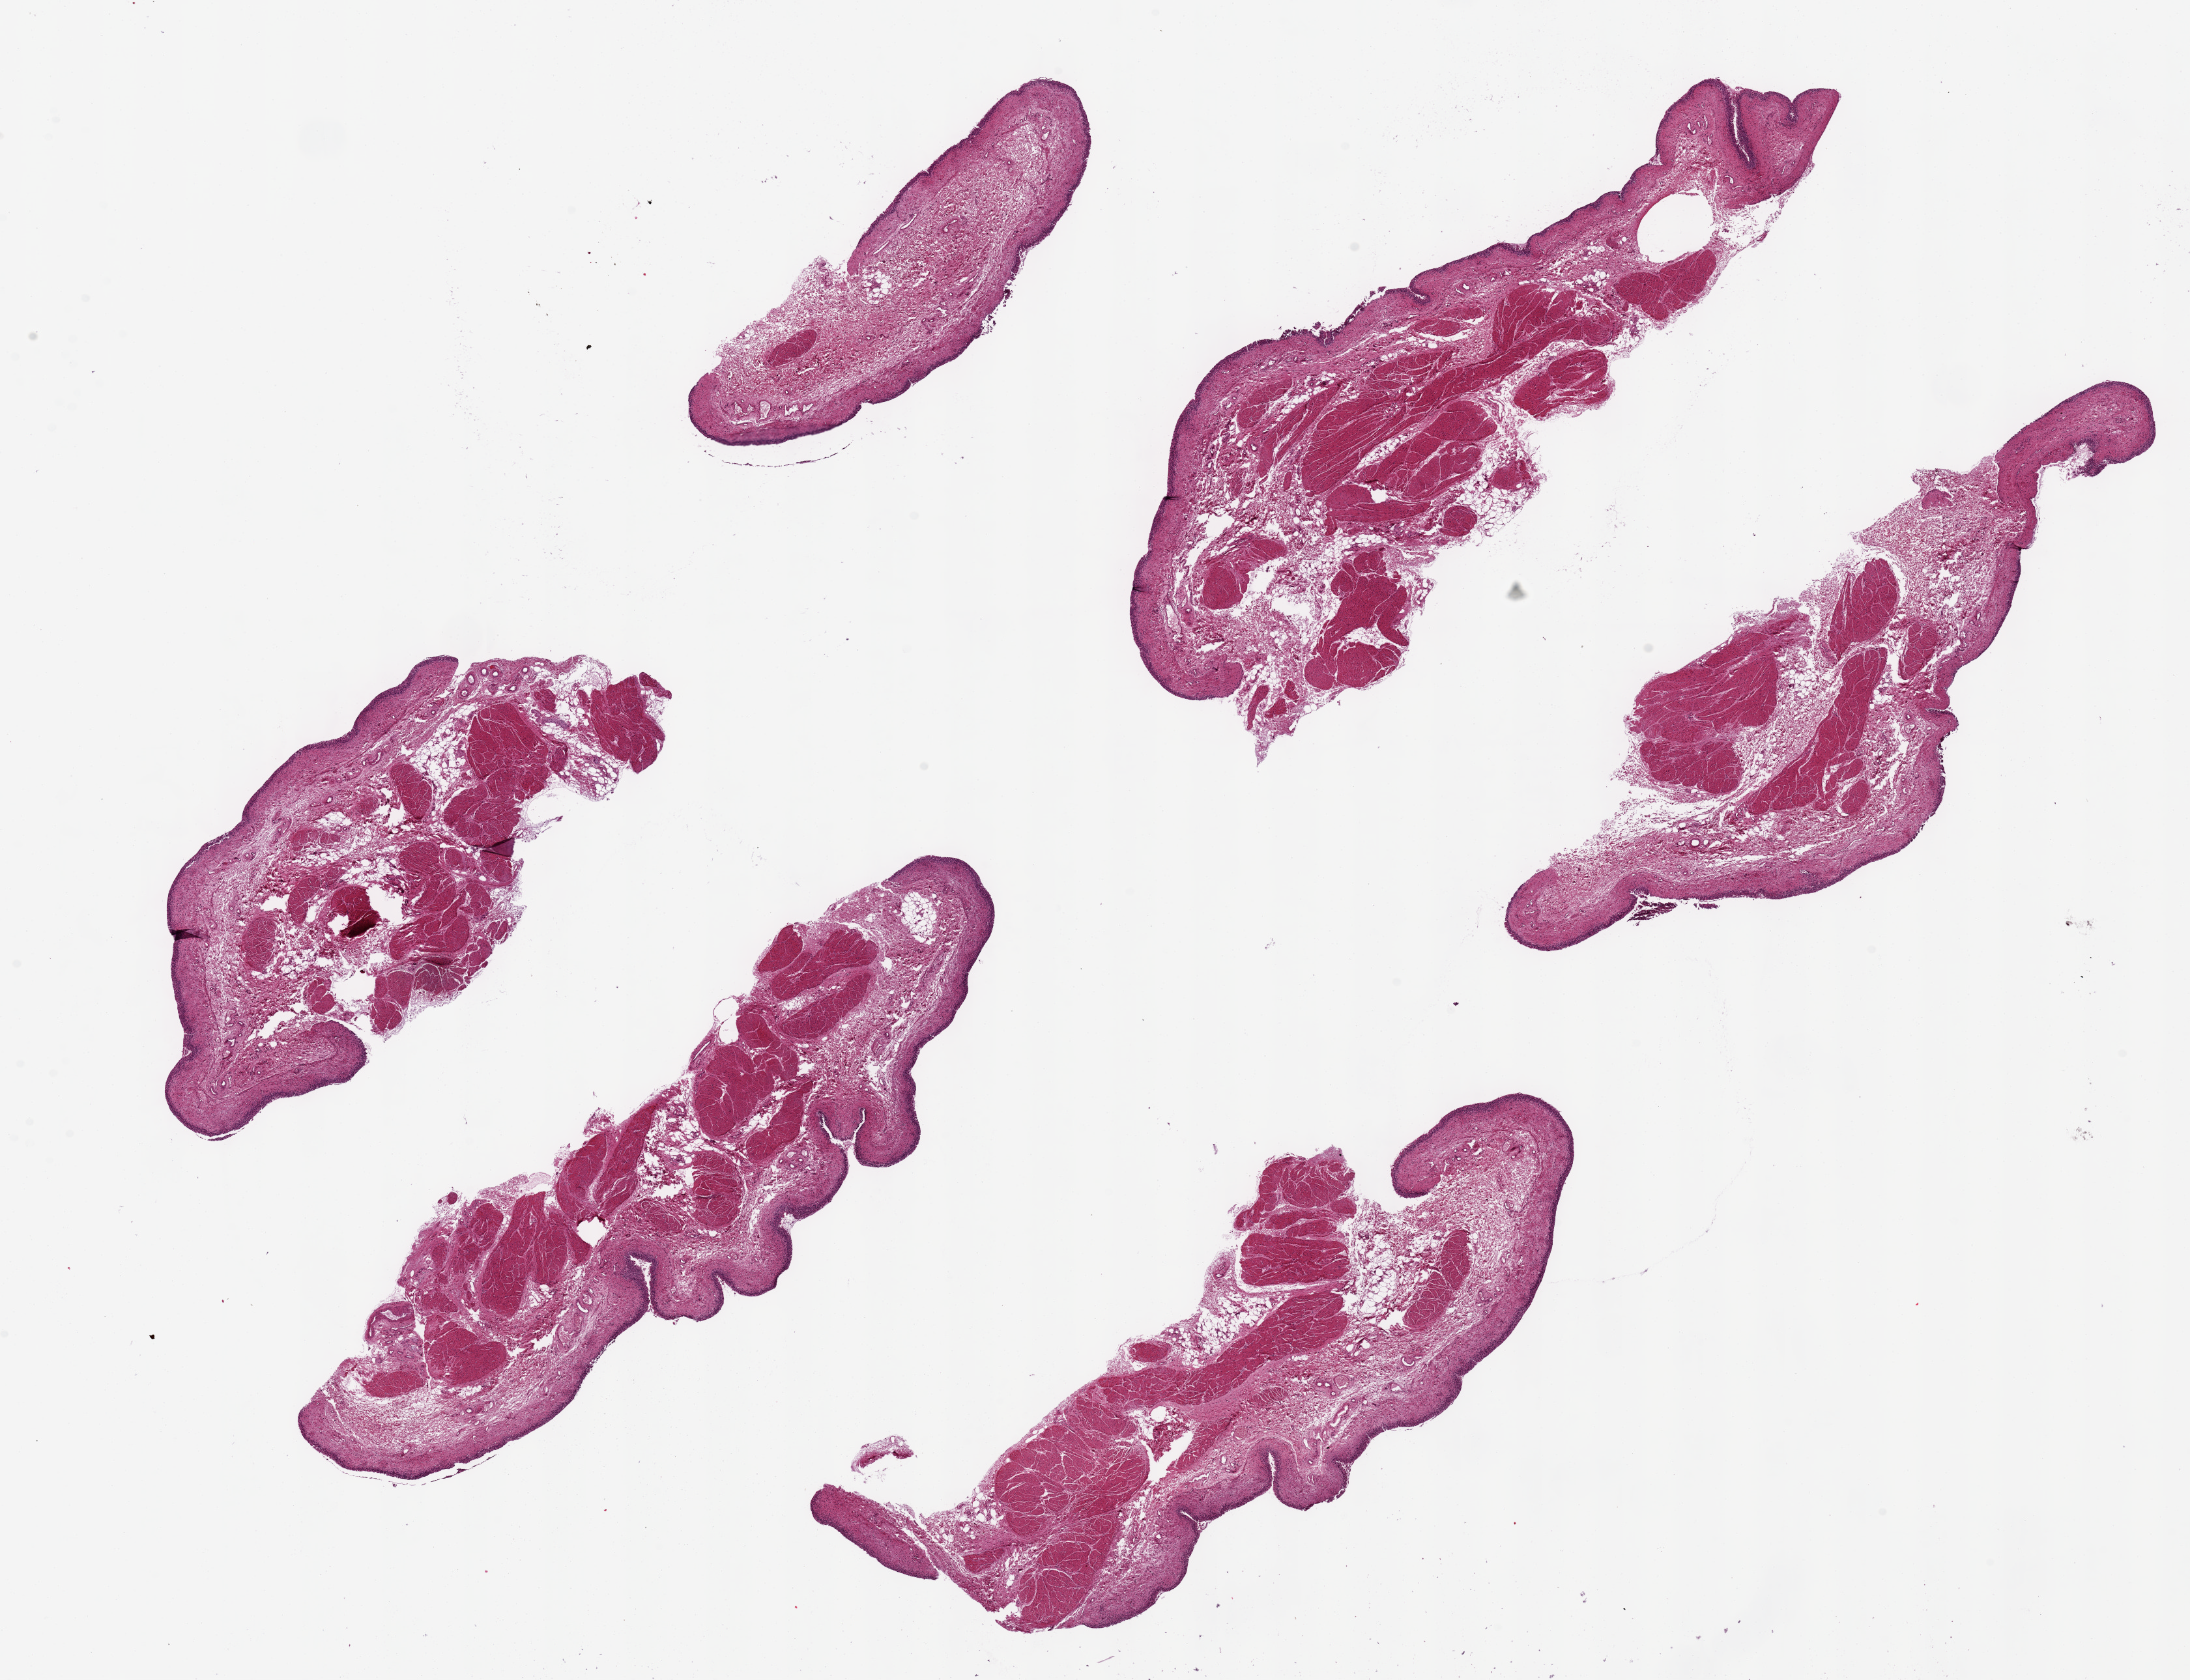
Digitized haematoxylin and eosin-stained section, low-resolution overview of the scanned area, about 26.6 x 20.4 mm (from a 20x scan). PAXgene-fixed, paraffin-embedded tissue. Sampled site (target tissue): urinary bladder. Tissue donor sample. Donor: female.
Review note (as recorded): 6 ~10x3mm pieces. Urothelium partially sloughed, variably preserved, 1-2 % of thickness.